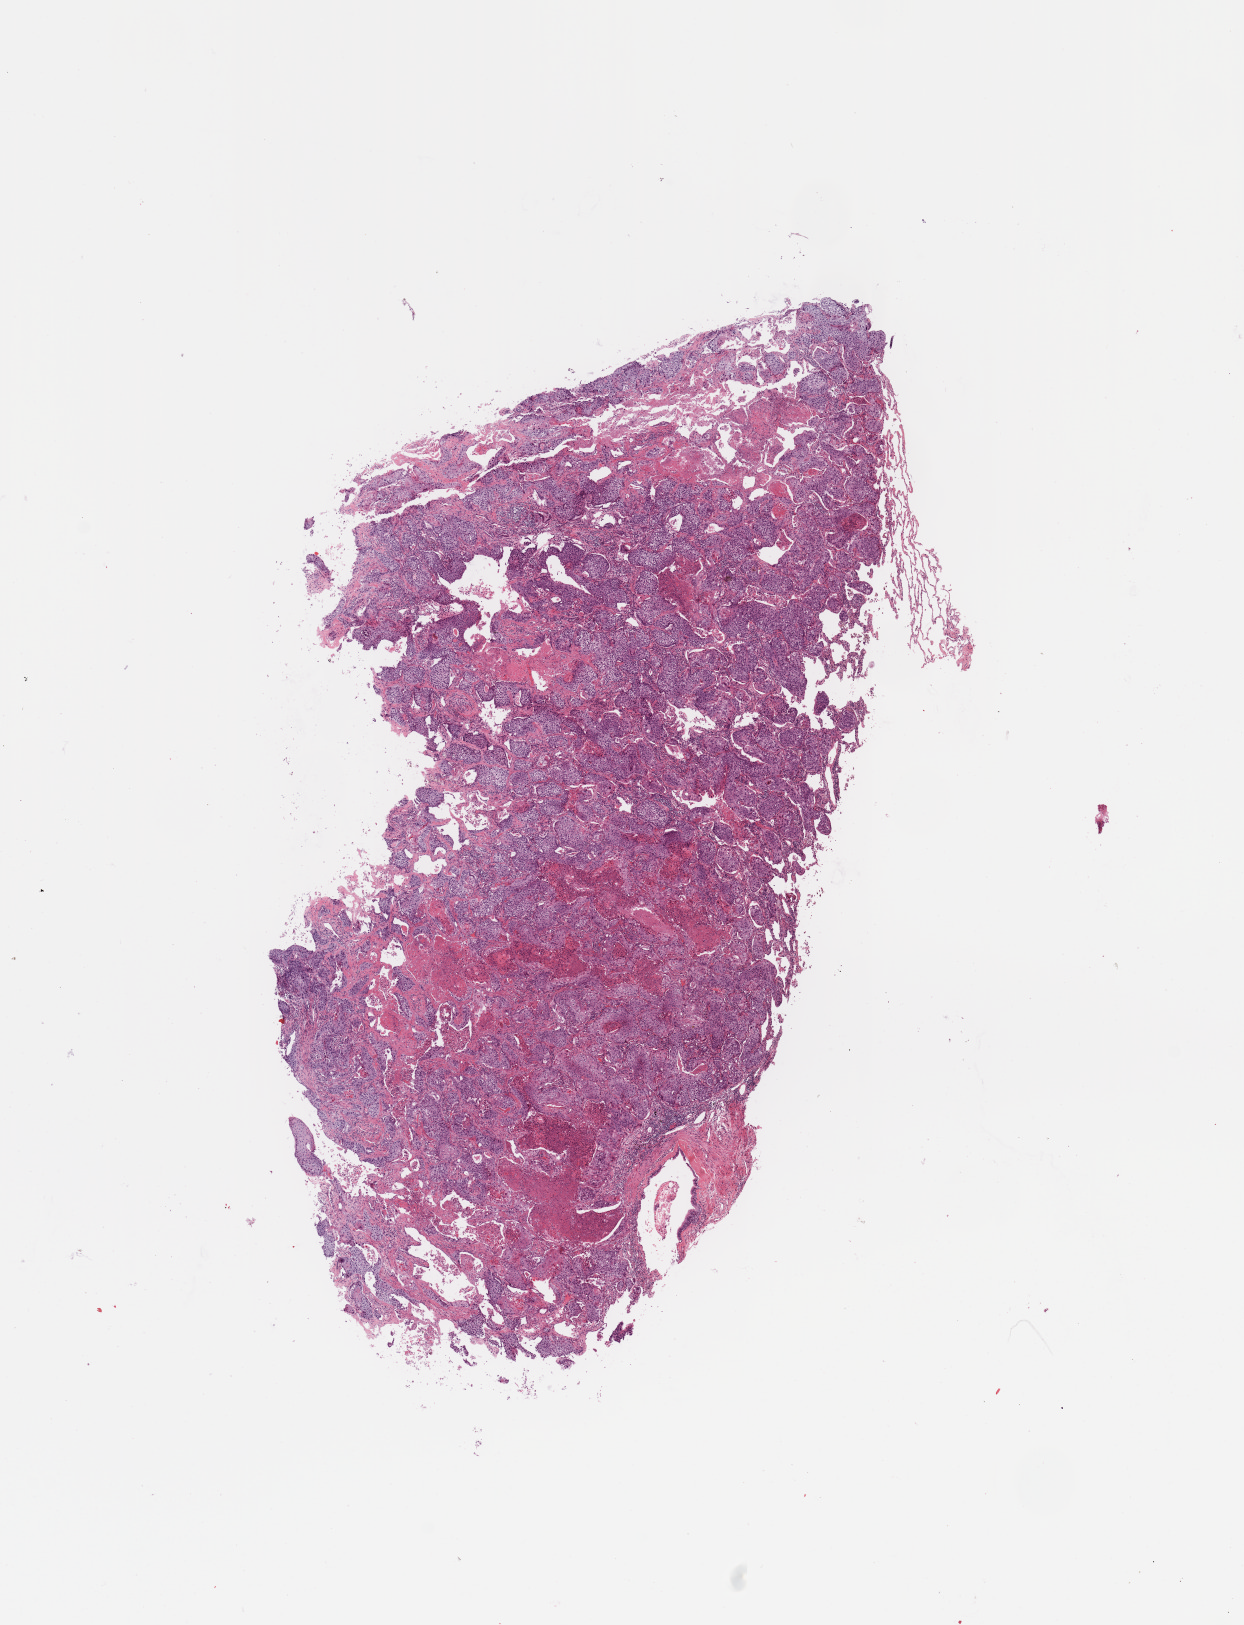
H&E whole-slide image — a low-resolution overview of the entire scanned area, about 9.8 x 12.9 mm; tumour tissue sample, sampled site: lung. Patient: male, age 65 years. Pathologist review of this section (percent, as recorded): tumour nuclei 65%, necrosis 15%.
Diagnosis: Squamous cell carcinoma, NOS.